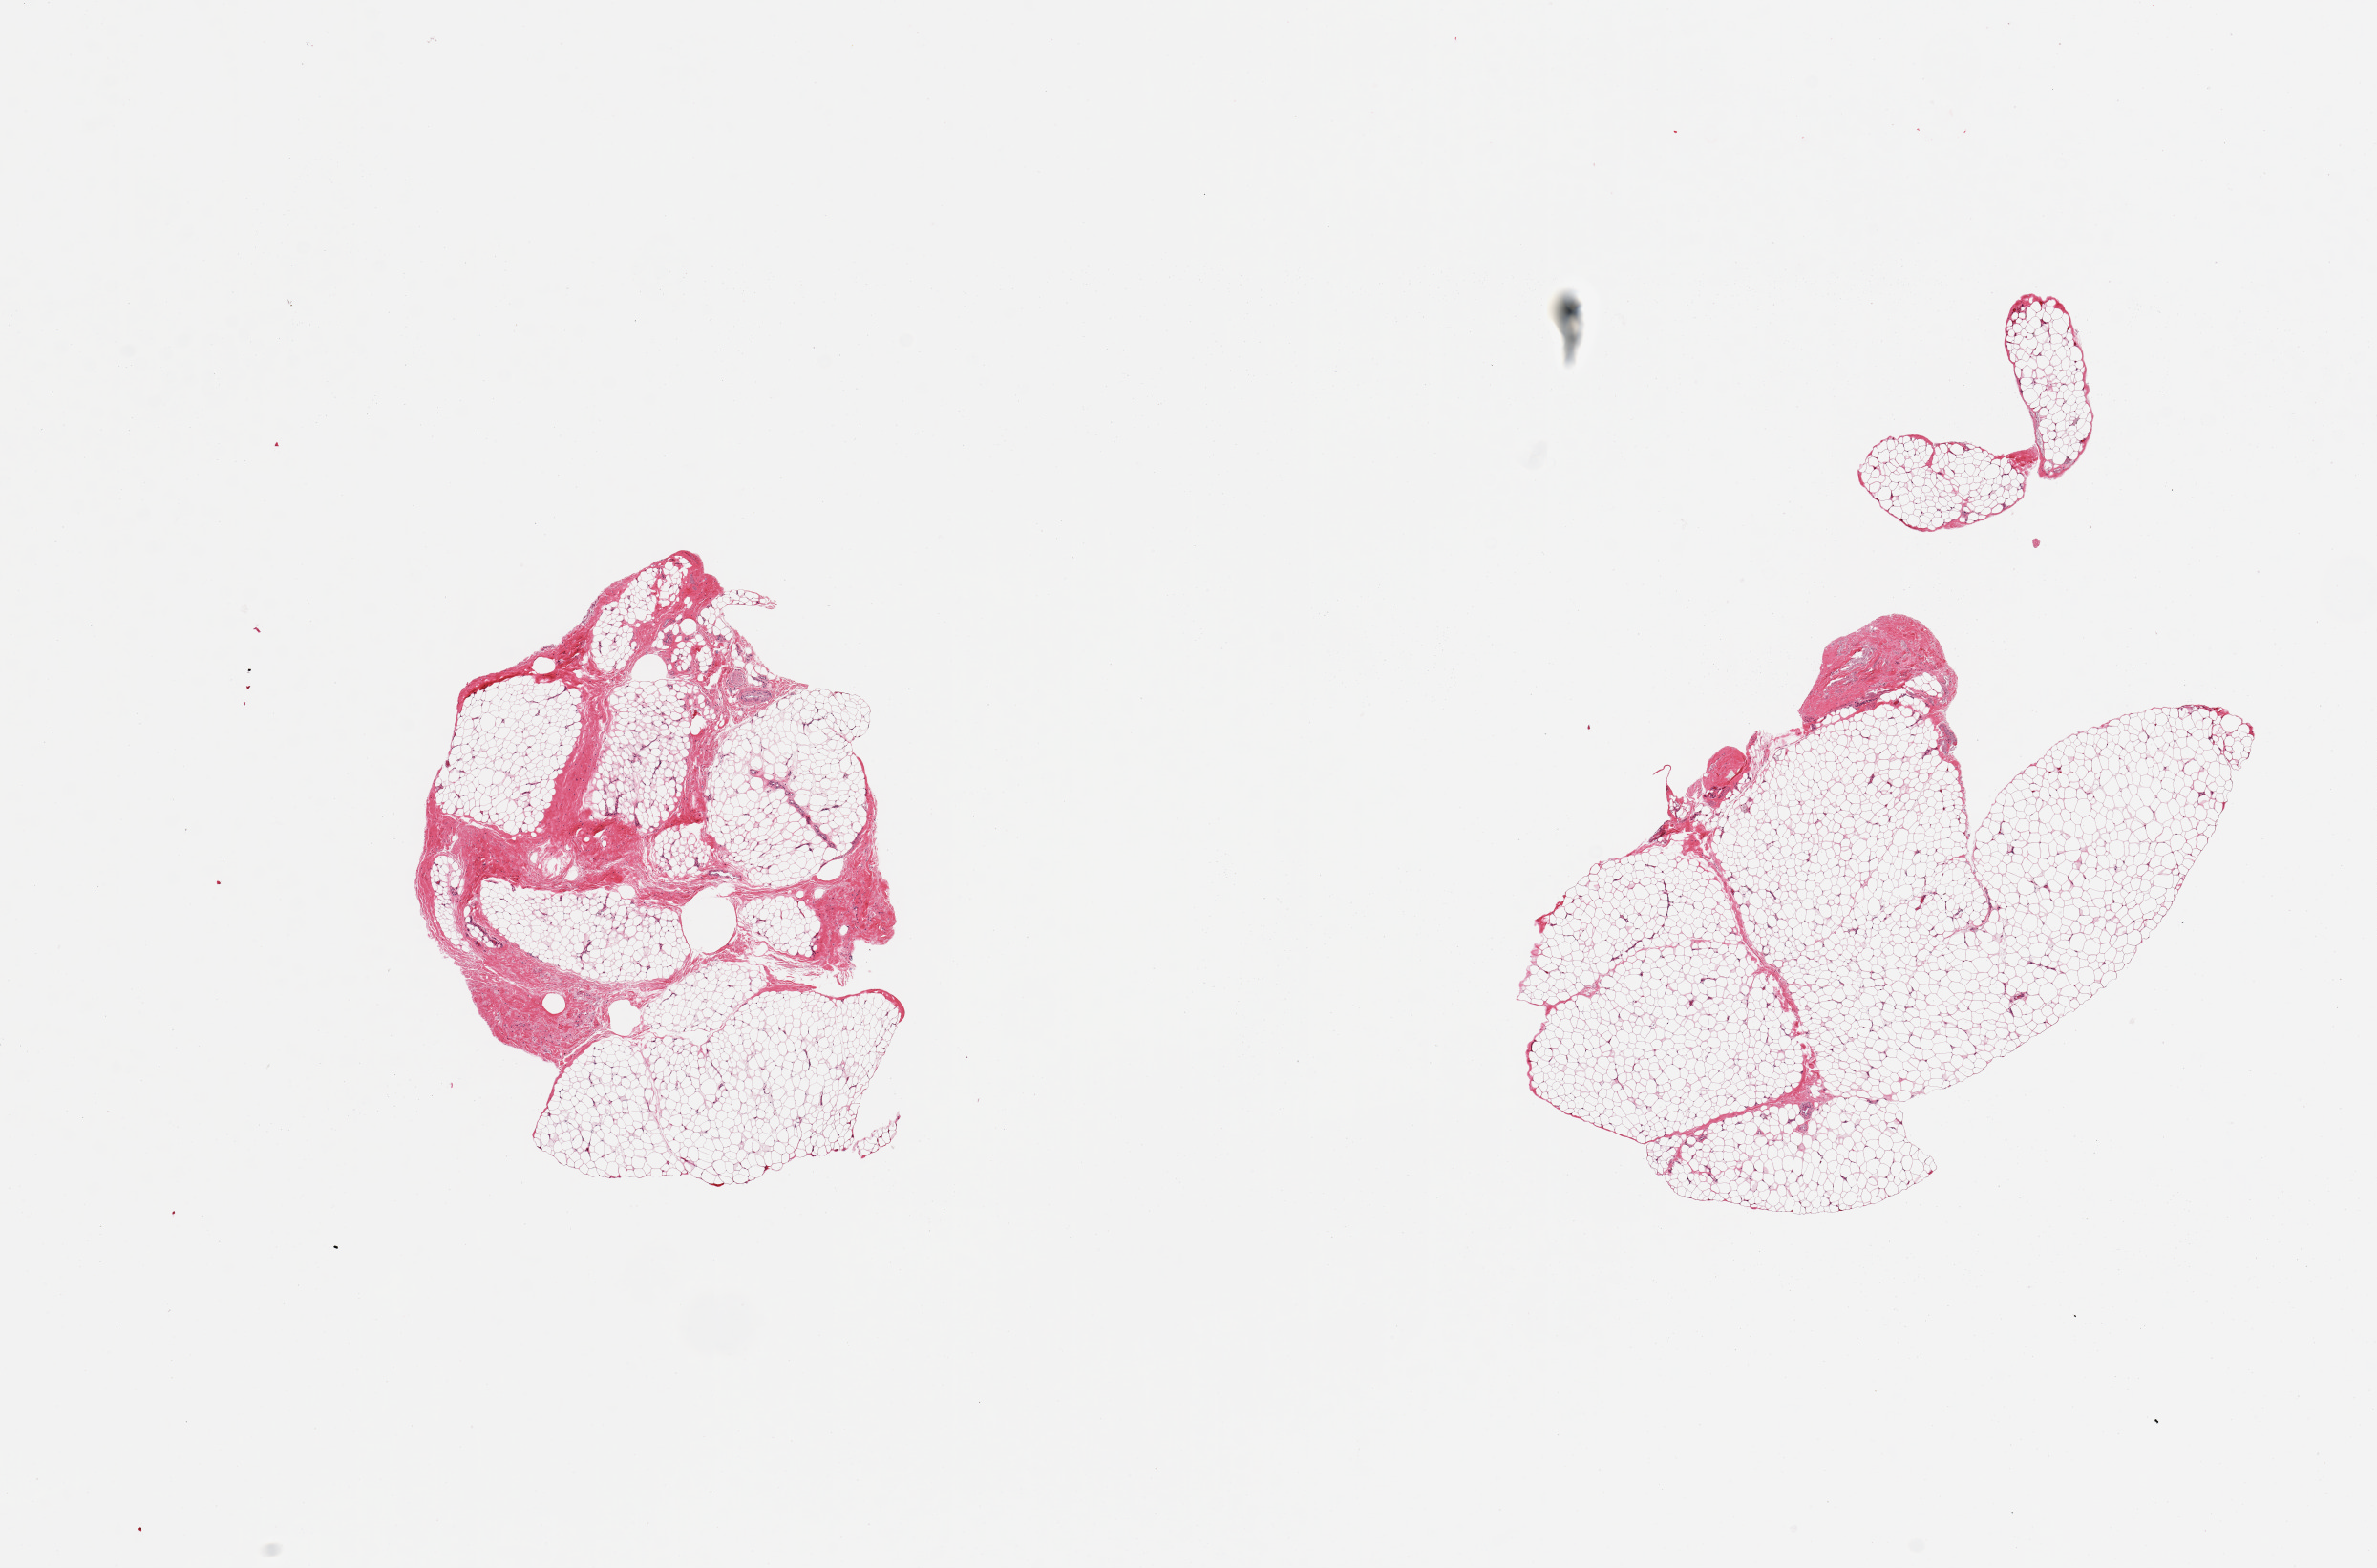
Digitized H&E-stained section — shown as a low-resolution overview of the whole scanned area (about 19.7 x 13.0 mm, acquisition: 20x scan); PAXgene-fixed paraffin-embedded (PFPE) section; target tissue: adipose tissue; tissue donor sample. Donor: male.
Review note (as recorded): 2 pieces, ~20% fascia/fibrous tissue.